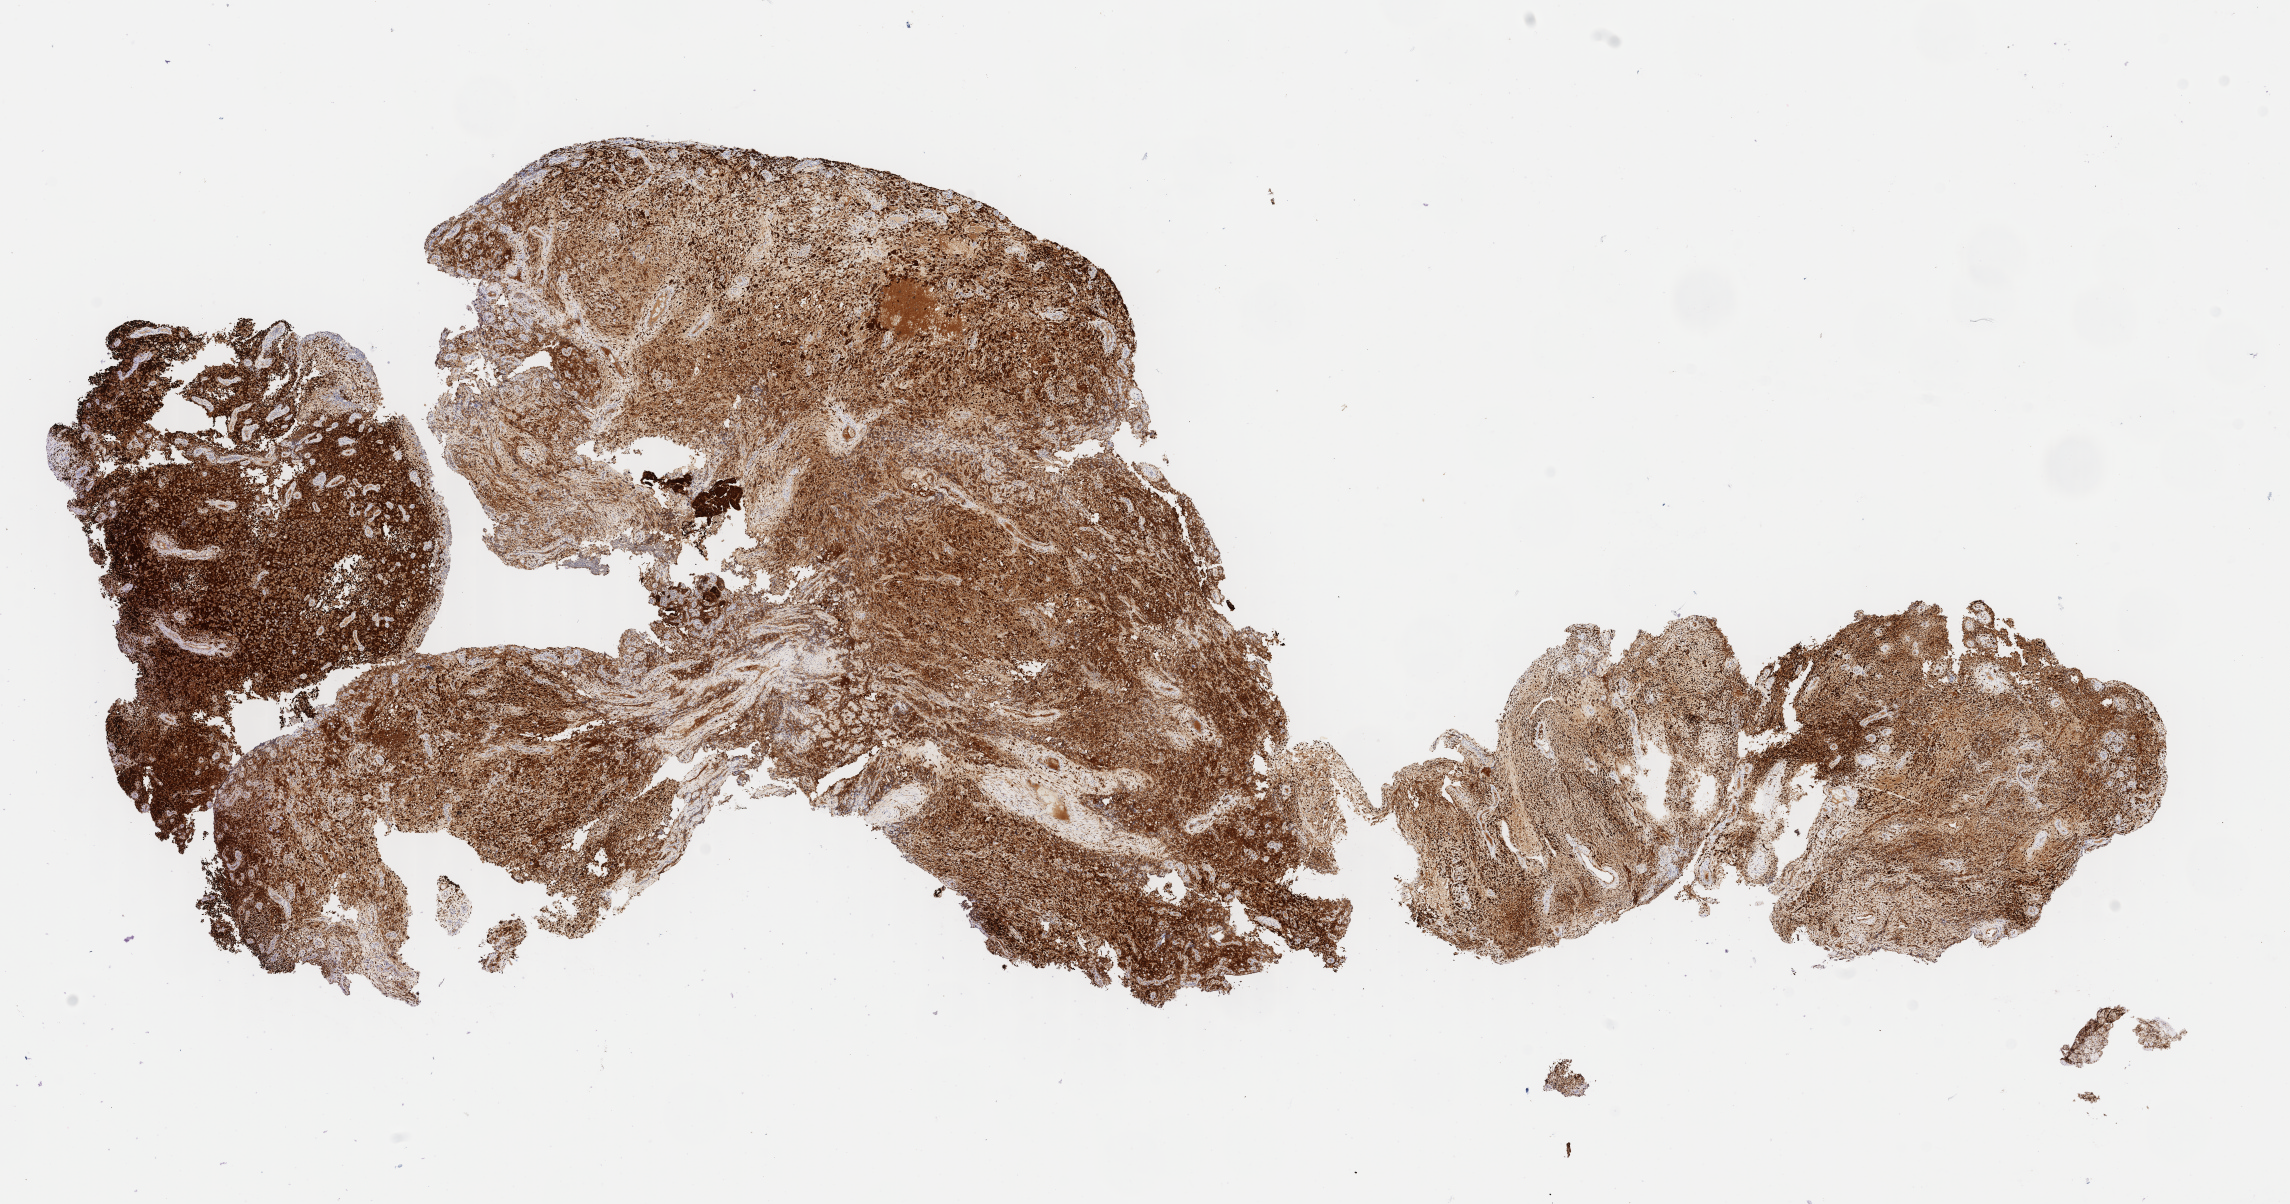
Immunohistochemistry (IHC) whole-slide image stained for p16 (p16INK4a), low-resolution overview of the scanned area, about 18.2 x 9.6 mm, specimen: tumor tissue, anatomic site: cervix. Patient female; aged 48.
Histologic diagnosis: Squamous cell carcinoma, NOS.